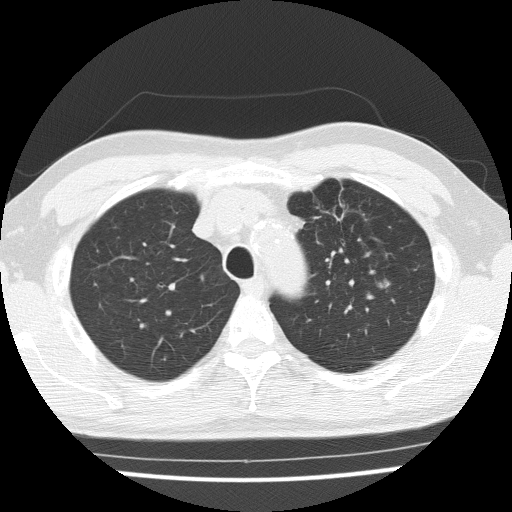
Chest CT (low-dose screening protocol), one axial image. Third screening round (two years after baseline). Lung window (W 1500 / L -600 HU). Lung (sharp) reconstruction kernel (FC51). 120 kVp. Slice 40 of 154 in the series. 512 × 512 image matrix. Male, age 65 years at enrolment.
Expert-annotated lung lesion, bounding box [x1, y1, x2, y2] px = [352, 267, 406, 312]. Reader record for this screening exam (exam-level; its link to the box is not recorded): non-calcified nodule or mass ≥4 mm, left upper lobe, 16 × 15 mm, poorly defined margins, soft tissue attenuation, pre-existing on the prior screen: yes; interval growth: yes. Official screen result: positive, other. Later outcome: lung cancer diagnosed 42 days after this screen — squamous cell carcinoma, NOS, left upper lobe, moderately differentiated (G2), stage IA (AJCC 6th edition), 25 mm at pathology.